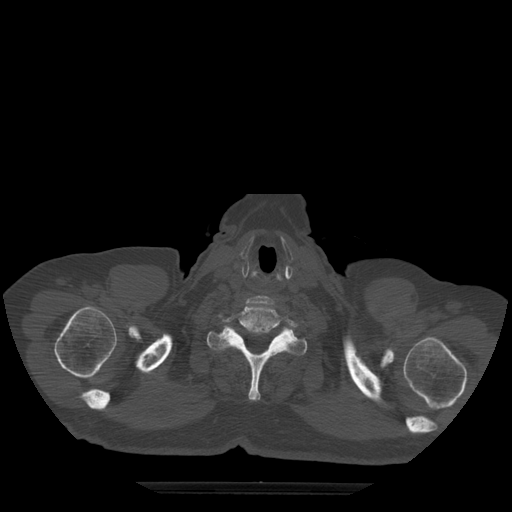
CT including the spine, one axial slice. Position 447 of 522 along the scan axis. Bone window (W 1800 / L 400 HU). 512 × 512 image matrix. Patient age 72 years. From the clinical record (not read from this slice): primary cancer: prostate.
Annotated regions visible in this slice (semi-automatically segmented with operator editing):
- T1 vertebra: bounding box (x1, y1, x2, y2) in pixels: (207, 326, 308, 401)